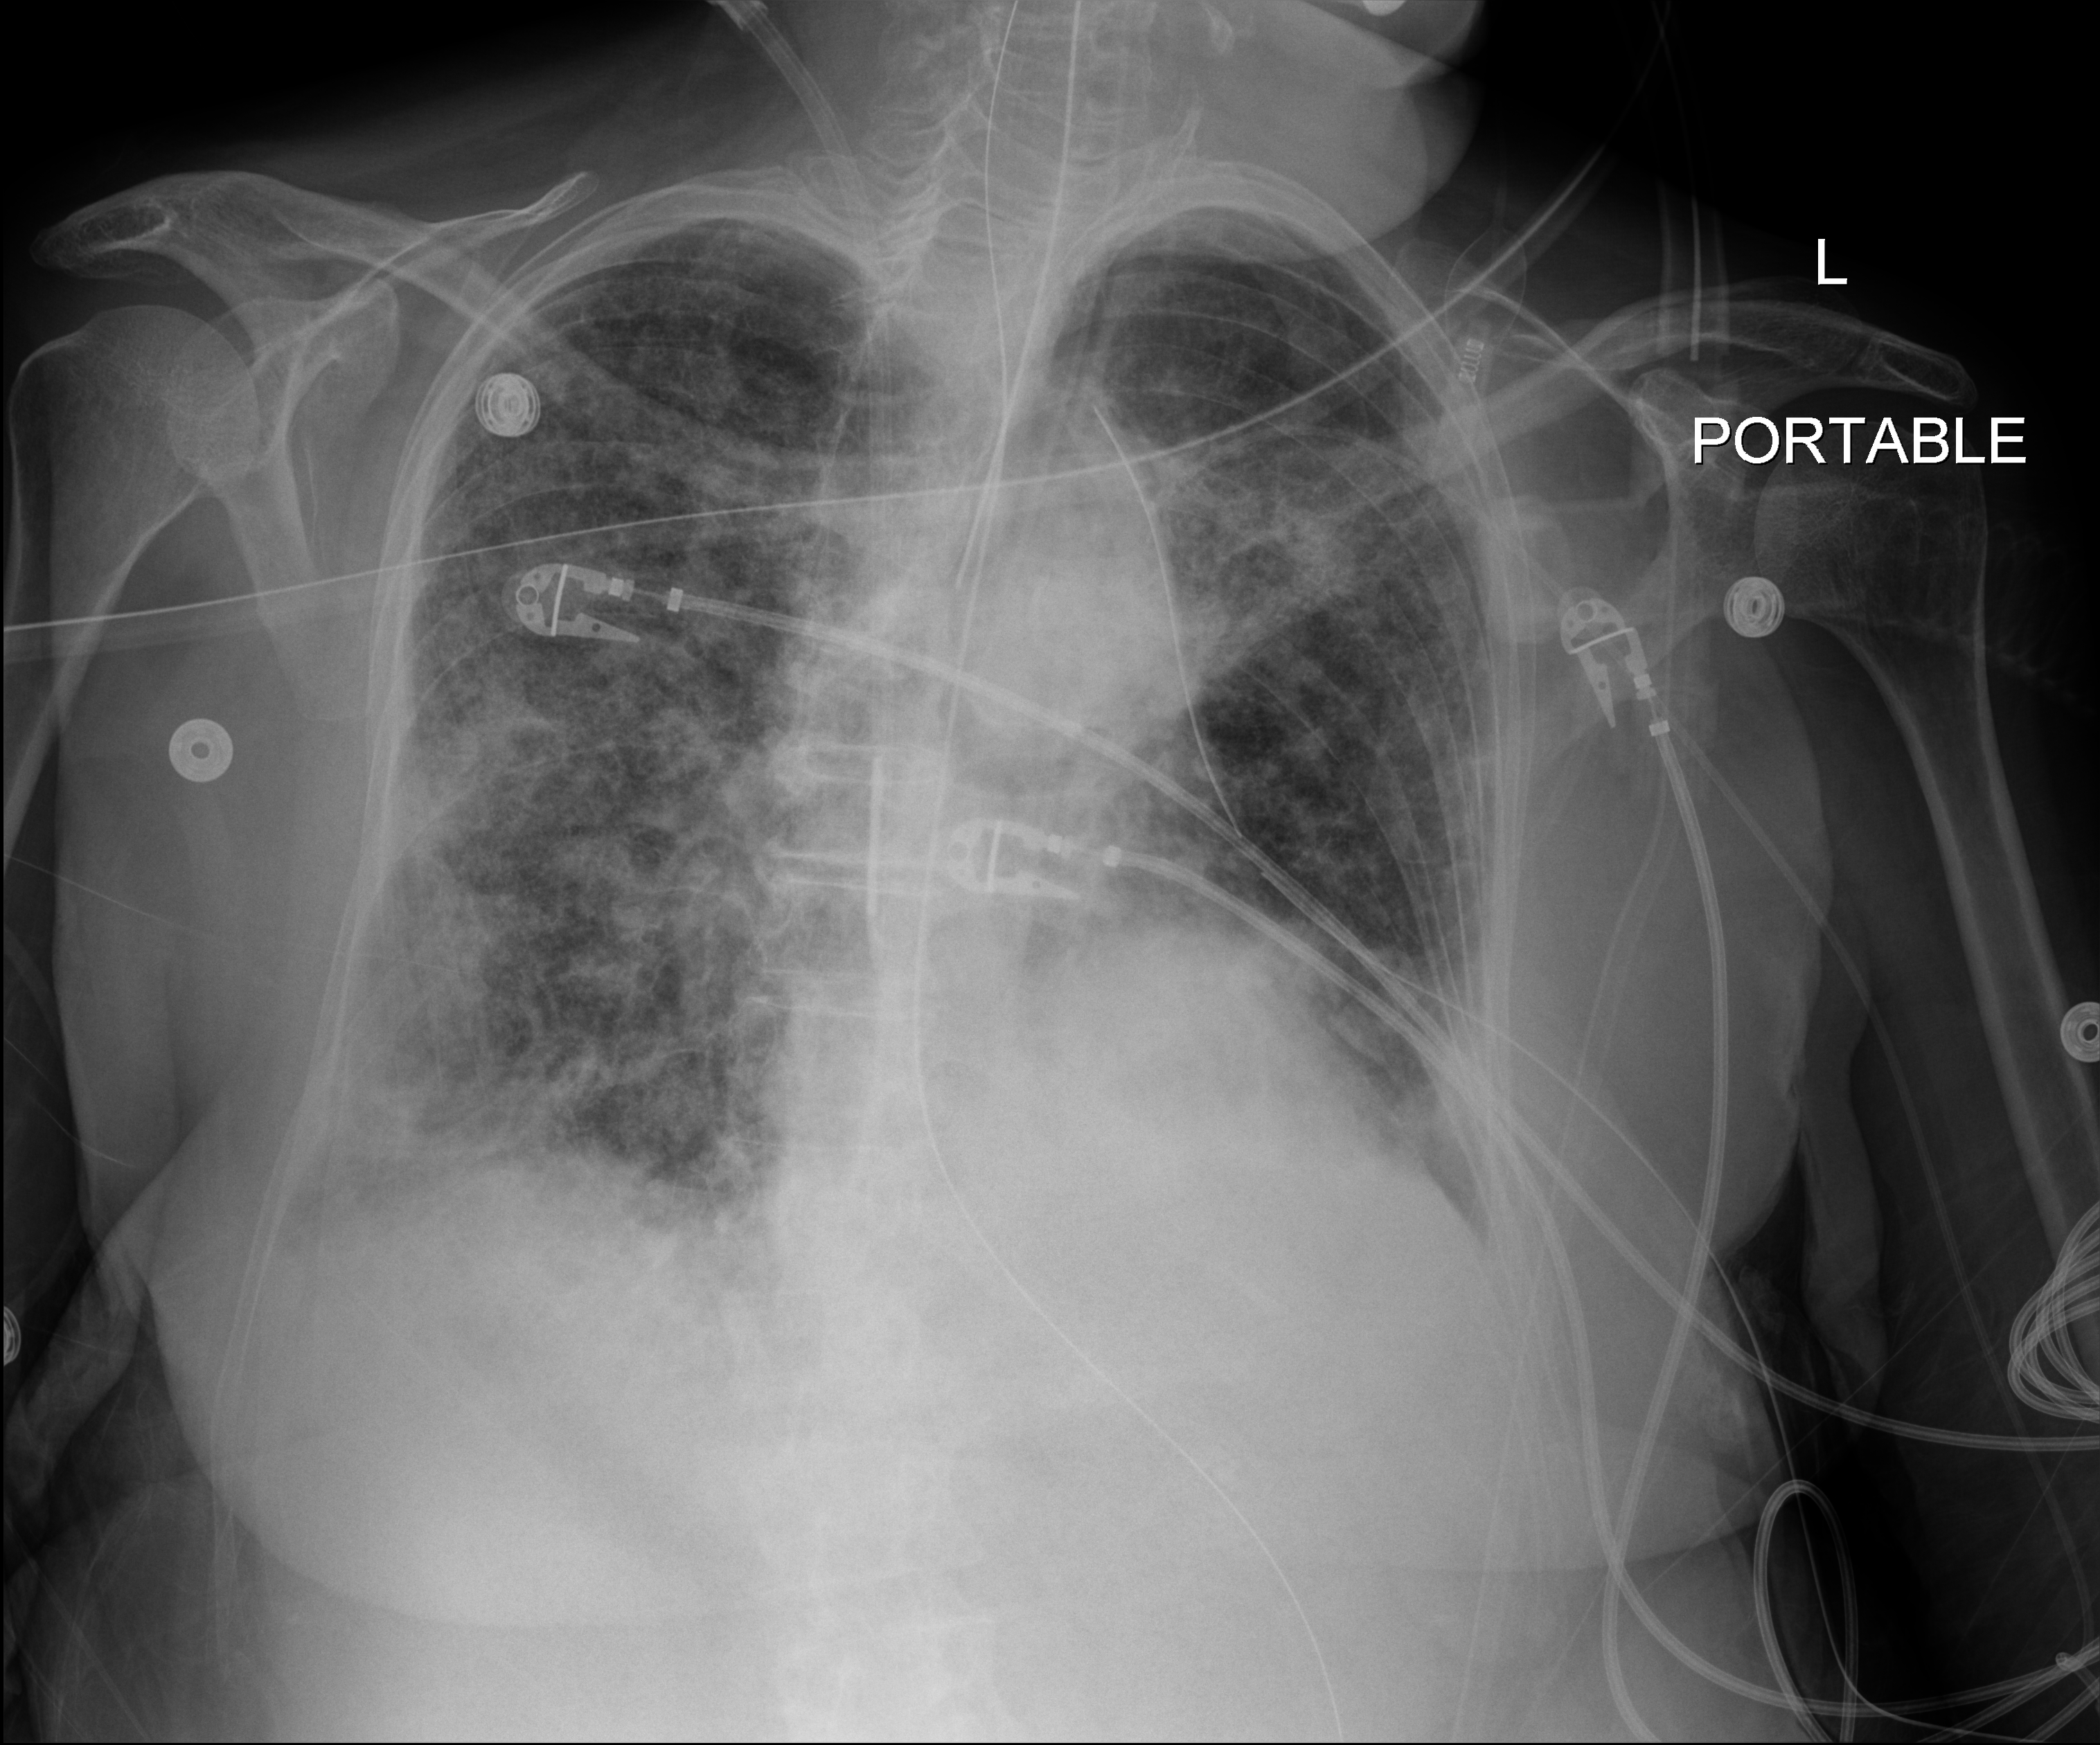
Chest X-ray (portable). Patient hospitalised with COVID-19; female, aged 75–90 years.
From the hospital-stay record, not from the radiograph (when in the stay this image was taken is not recorded):
- mechanically ventilated during this hospital stay: yes
- admitted to intensive care during this hospital stay: yes
- length of hospital stay: 70 days